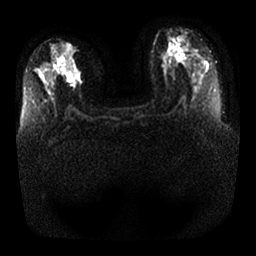
Breast MRI, one axial slice; diffusion-weighted series; image 2 of 4 stored at this slice position (different b-values; order by instance number); 1.5 T; 256 × 256 image matrix, field of view 350 × 350 mm. Female patient.
Structures marked on this image (expert manual segmentation):
- tumour on diffusion-weighted imaging: bounding box <65,47,81,83> (left, top, right, bottom; pixels)